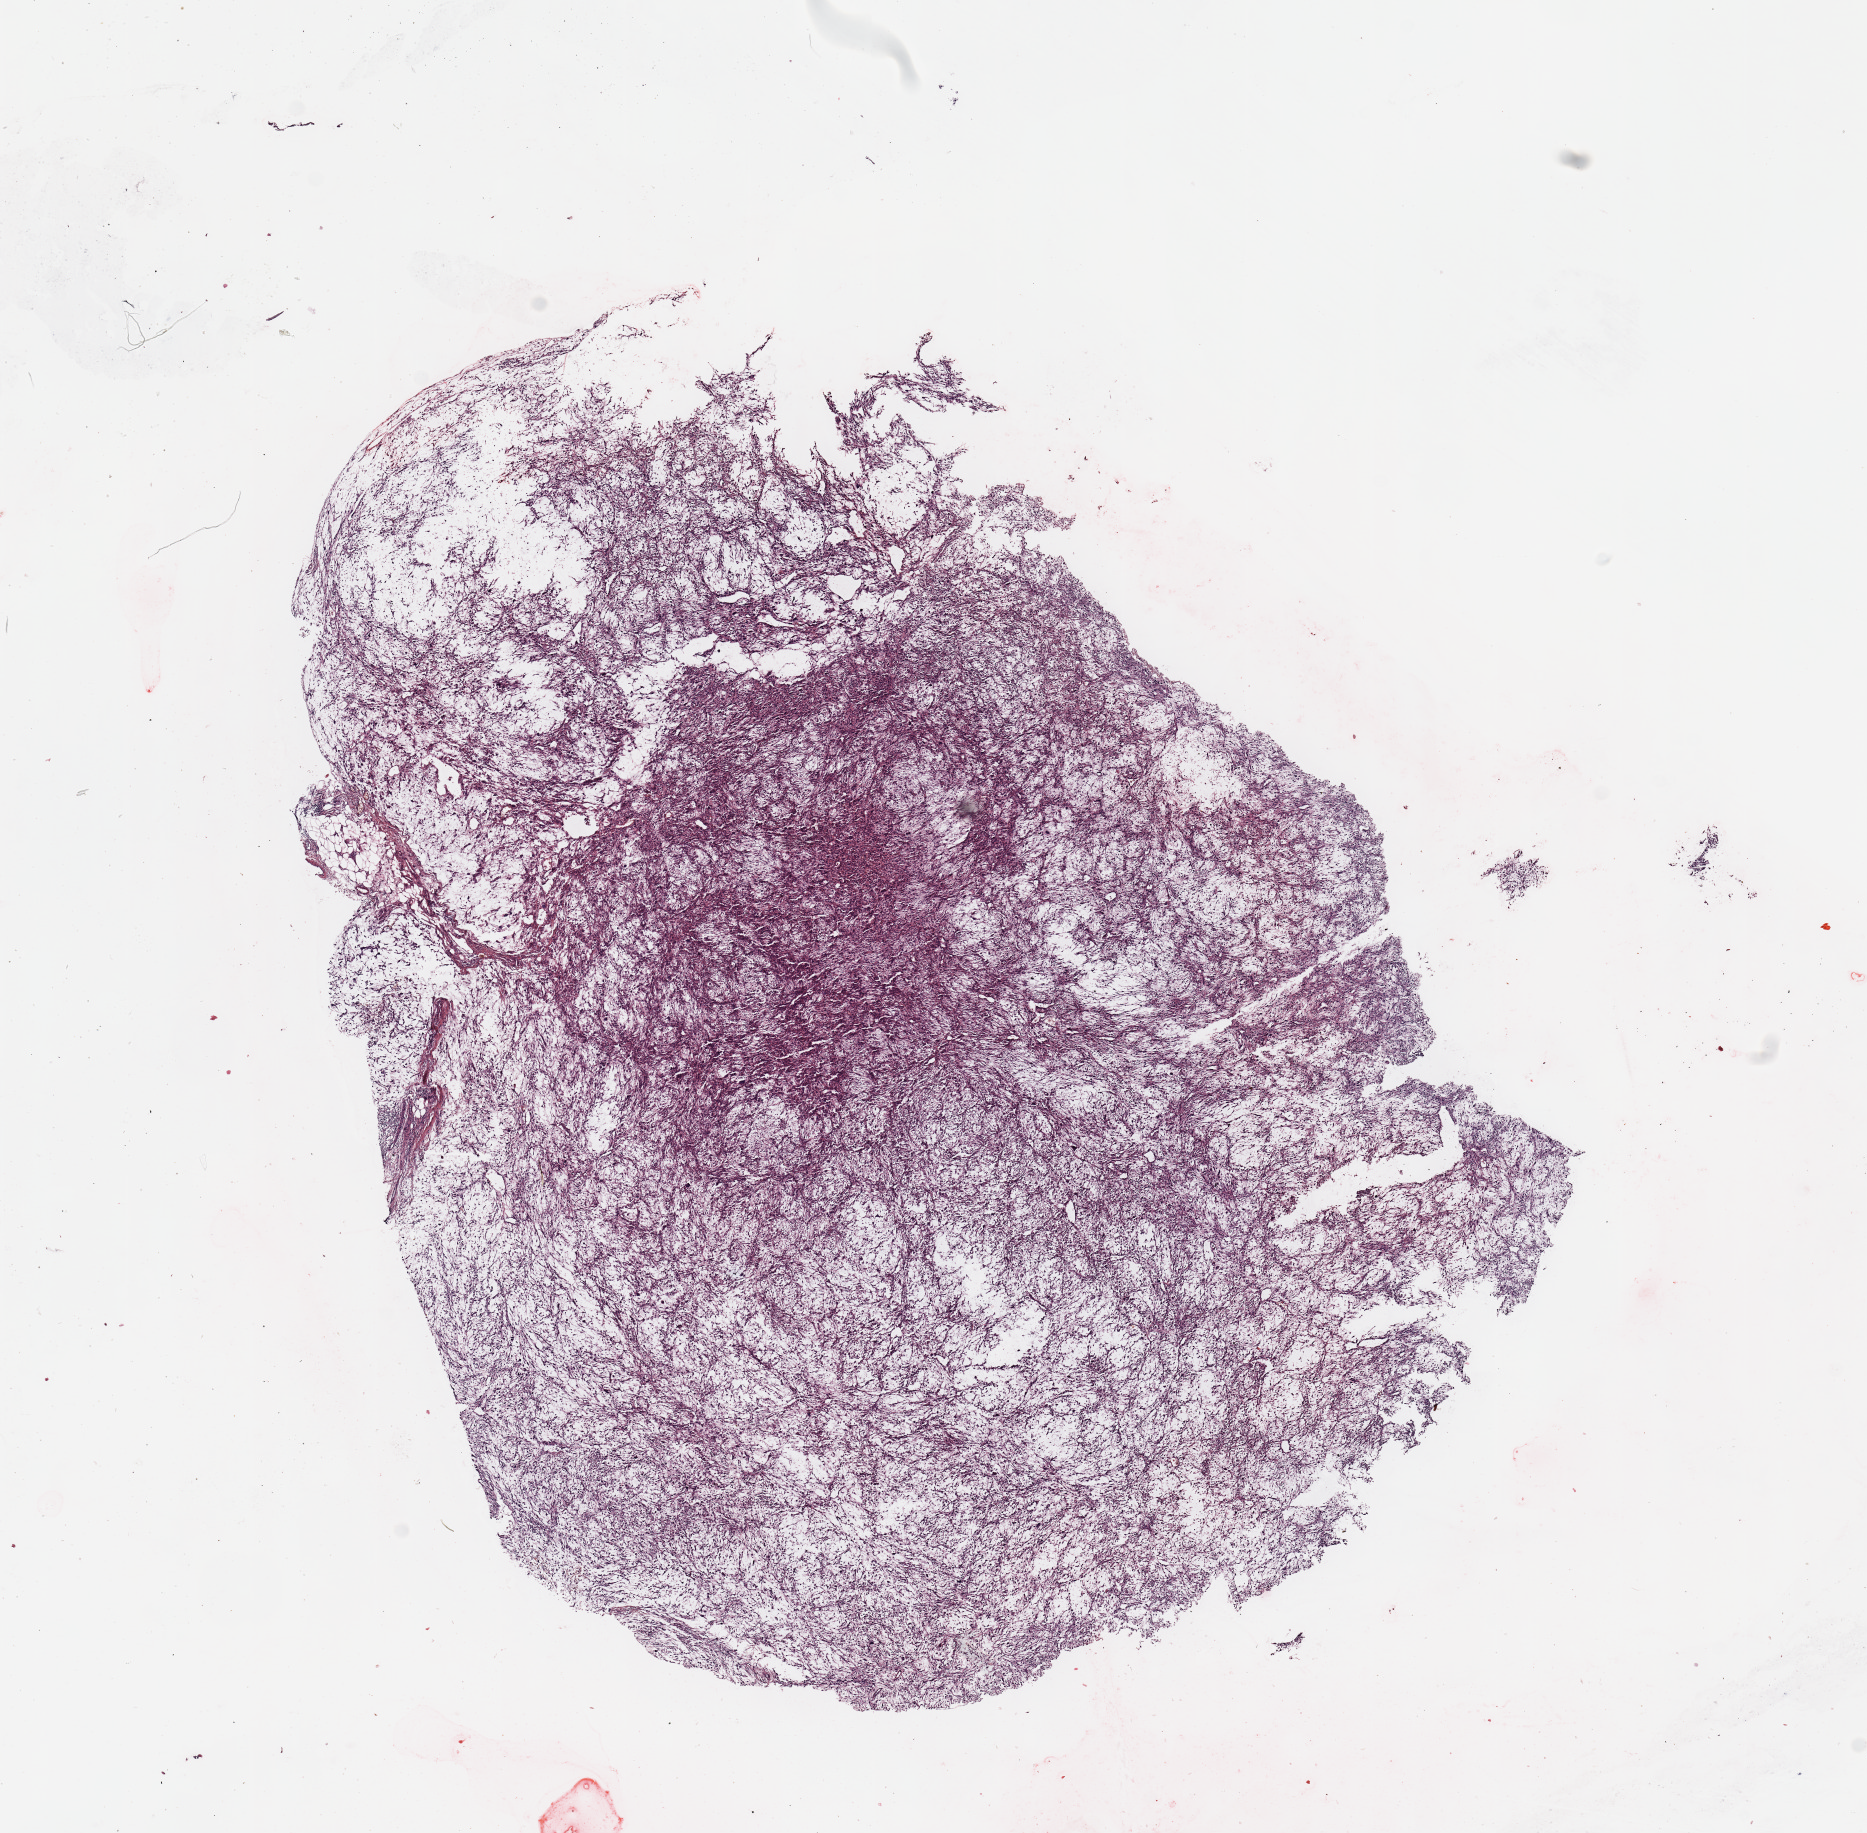
Whole-slide histology image, H&E, shown as a low-resolution overview of the whole scanned area (about 14.8 x 14.5 mm, from a 20x scan). Tumour tissue sample. Patient: male, age 72 years.
Primary tumour site (as recorded): upper extremity. Patient diagnosis (cohort enrolment): sarcoma (site not recorded at cohort level).